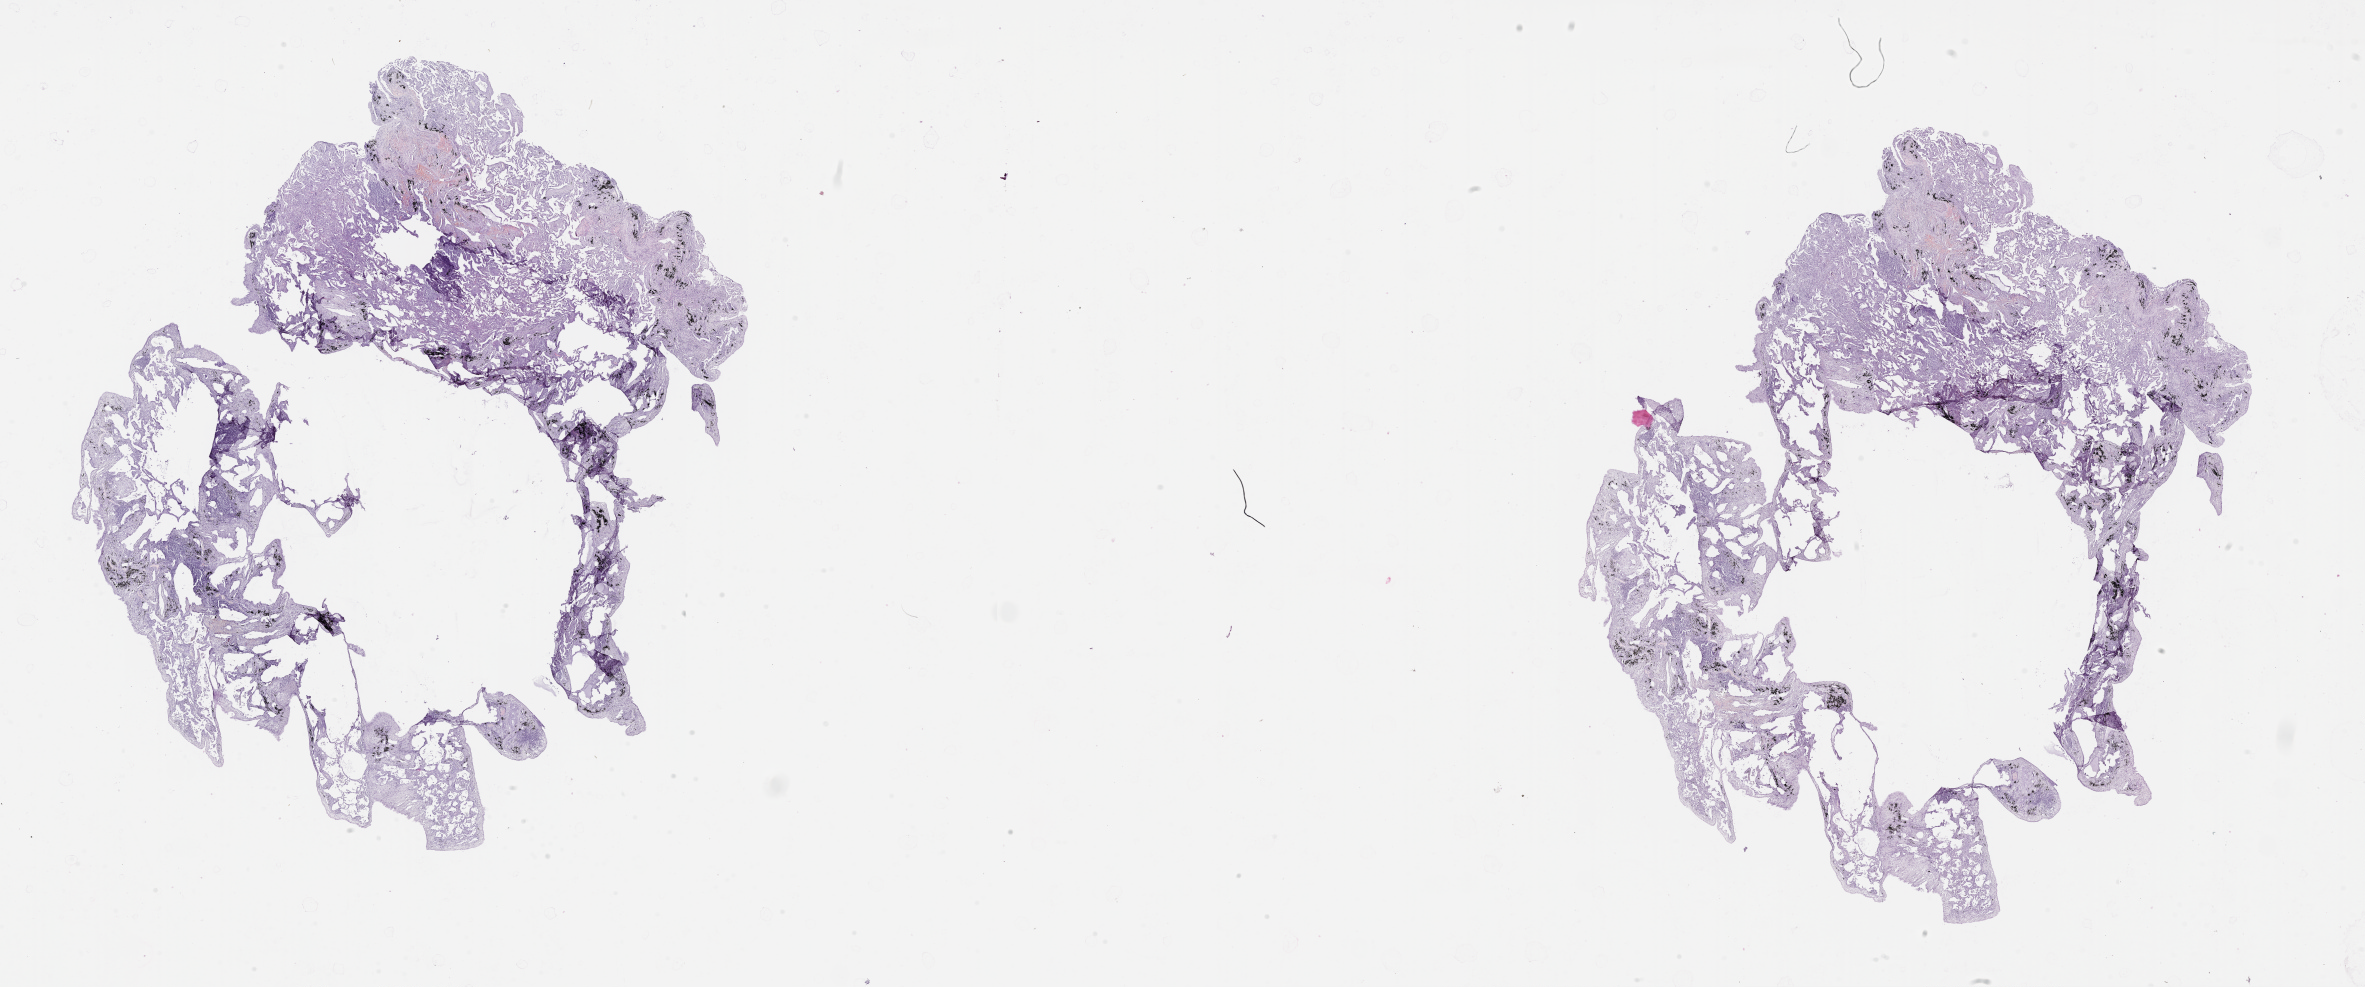
Whole-slide histology image, H&E, shown as a low-resolution overview of the whole scanned area (about 38.1 x 15.9 mm, slide scanned at 20x); normal (non-tumour) tissue sample, lung. 68-year-old male patient.
This section: normal (non-tumour) tissue from the same patient. Patient diagnosis (cohort enrolment): squamous cell carcinoma (lung).